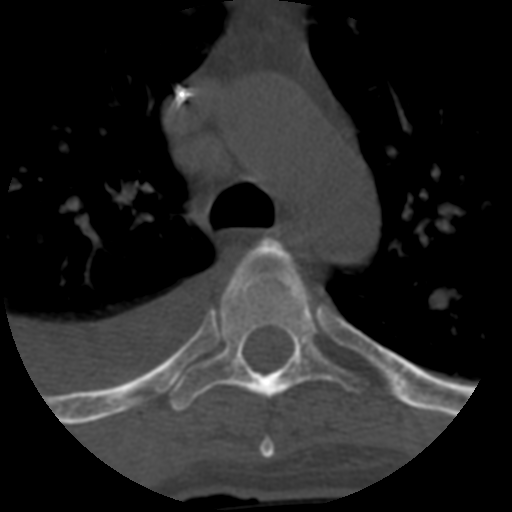
CT including the spine, one axial slice; position 458 of 708 along the scan axis; one of 3 acquisitions stored at this slice position; bone window (W 1800 / L 400 HU); 1.25 mm slice thickness; 512 × 512 image matrix, field of view 160 × 160 mm. Patient age 55 years. Case-level facts recorded for this patient, not image findings: primary cancer: colon; vertebrae with lytic lesions (as recorded): T12, L1, L5.
Outlined on this slice (semi-automatically segmented with operator editing):
- T4 vertebra: box from (x=239, y=237) to (x=295, y=459) px
- T5 vertebra: (x=170, y=247)–(x=367, y=411)